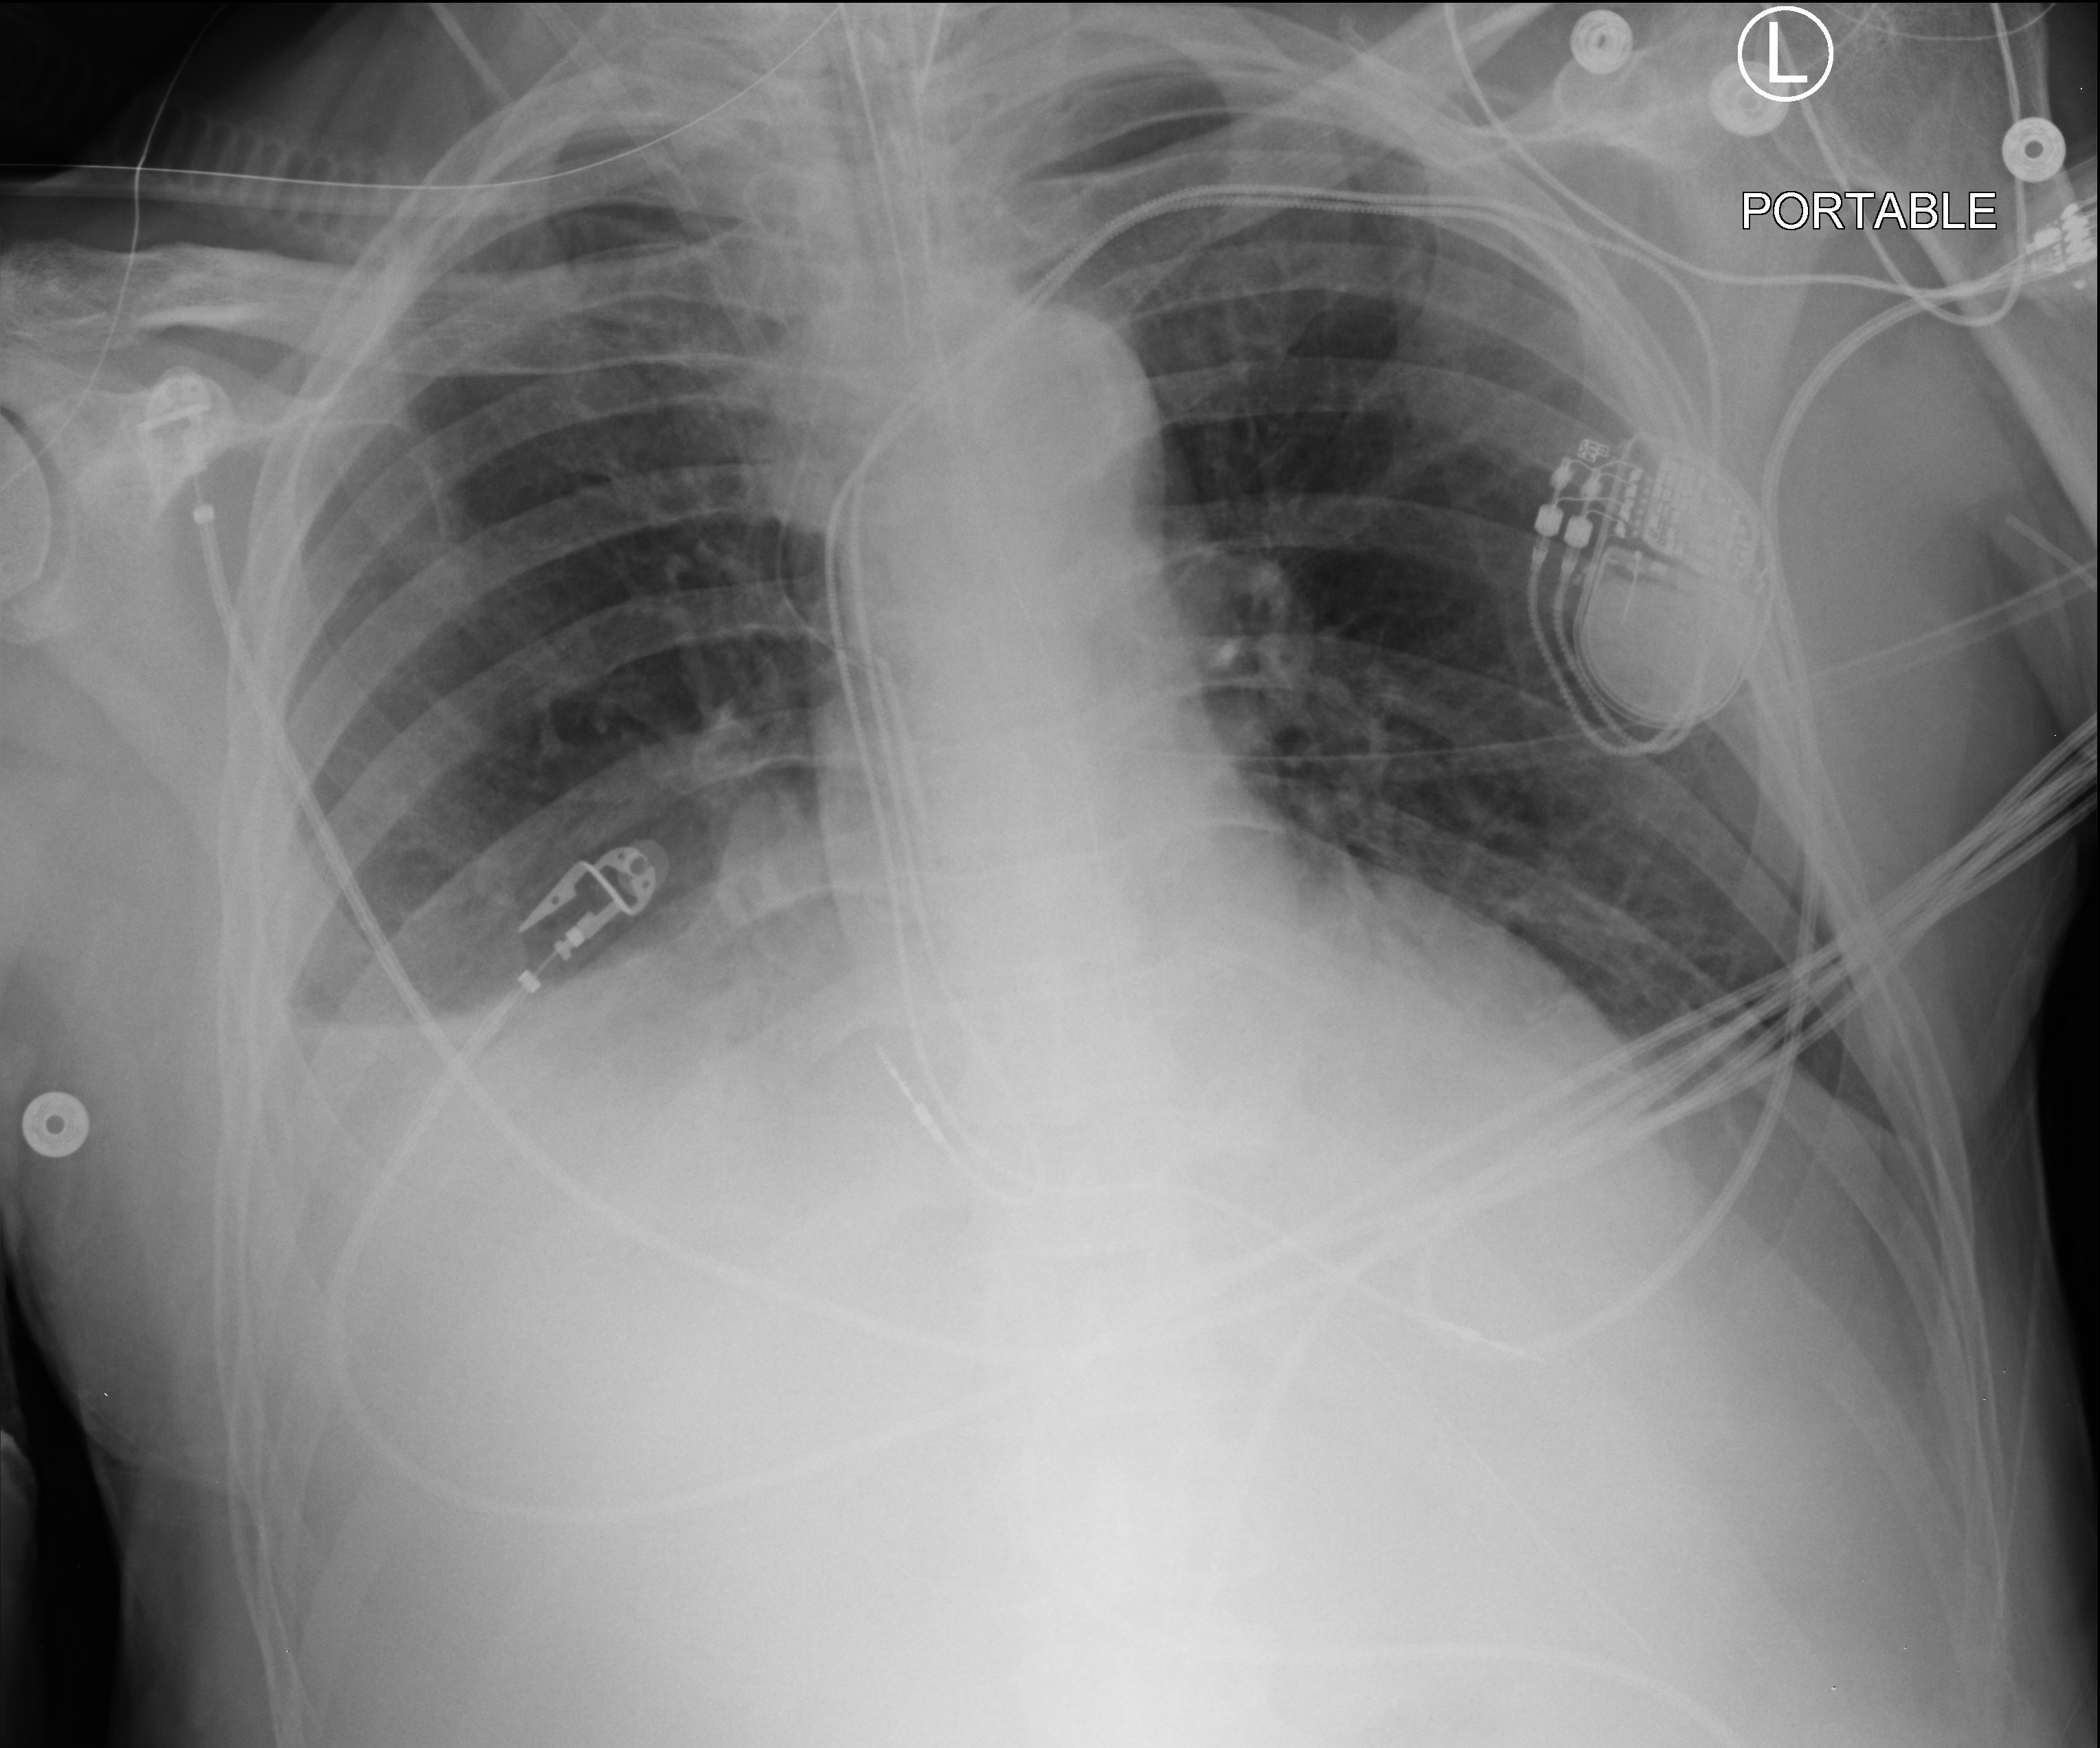
Bedside chest radiograph (computed radiography); anteroposterior (AP) projection. Male patient hospitalised with COVID-19, age 60–74 years.
From the hospital-stay record, not from the radiograph (when in the stay this image was taken is not recorded): admitted to intensive care during this hospital stay: yes; mechanically ventilated during this hospital stay: yes.